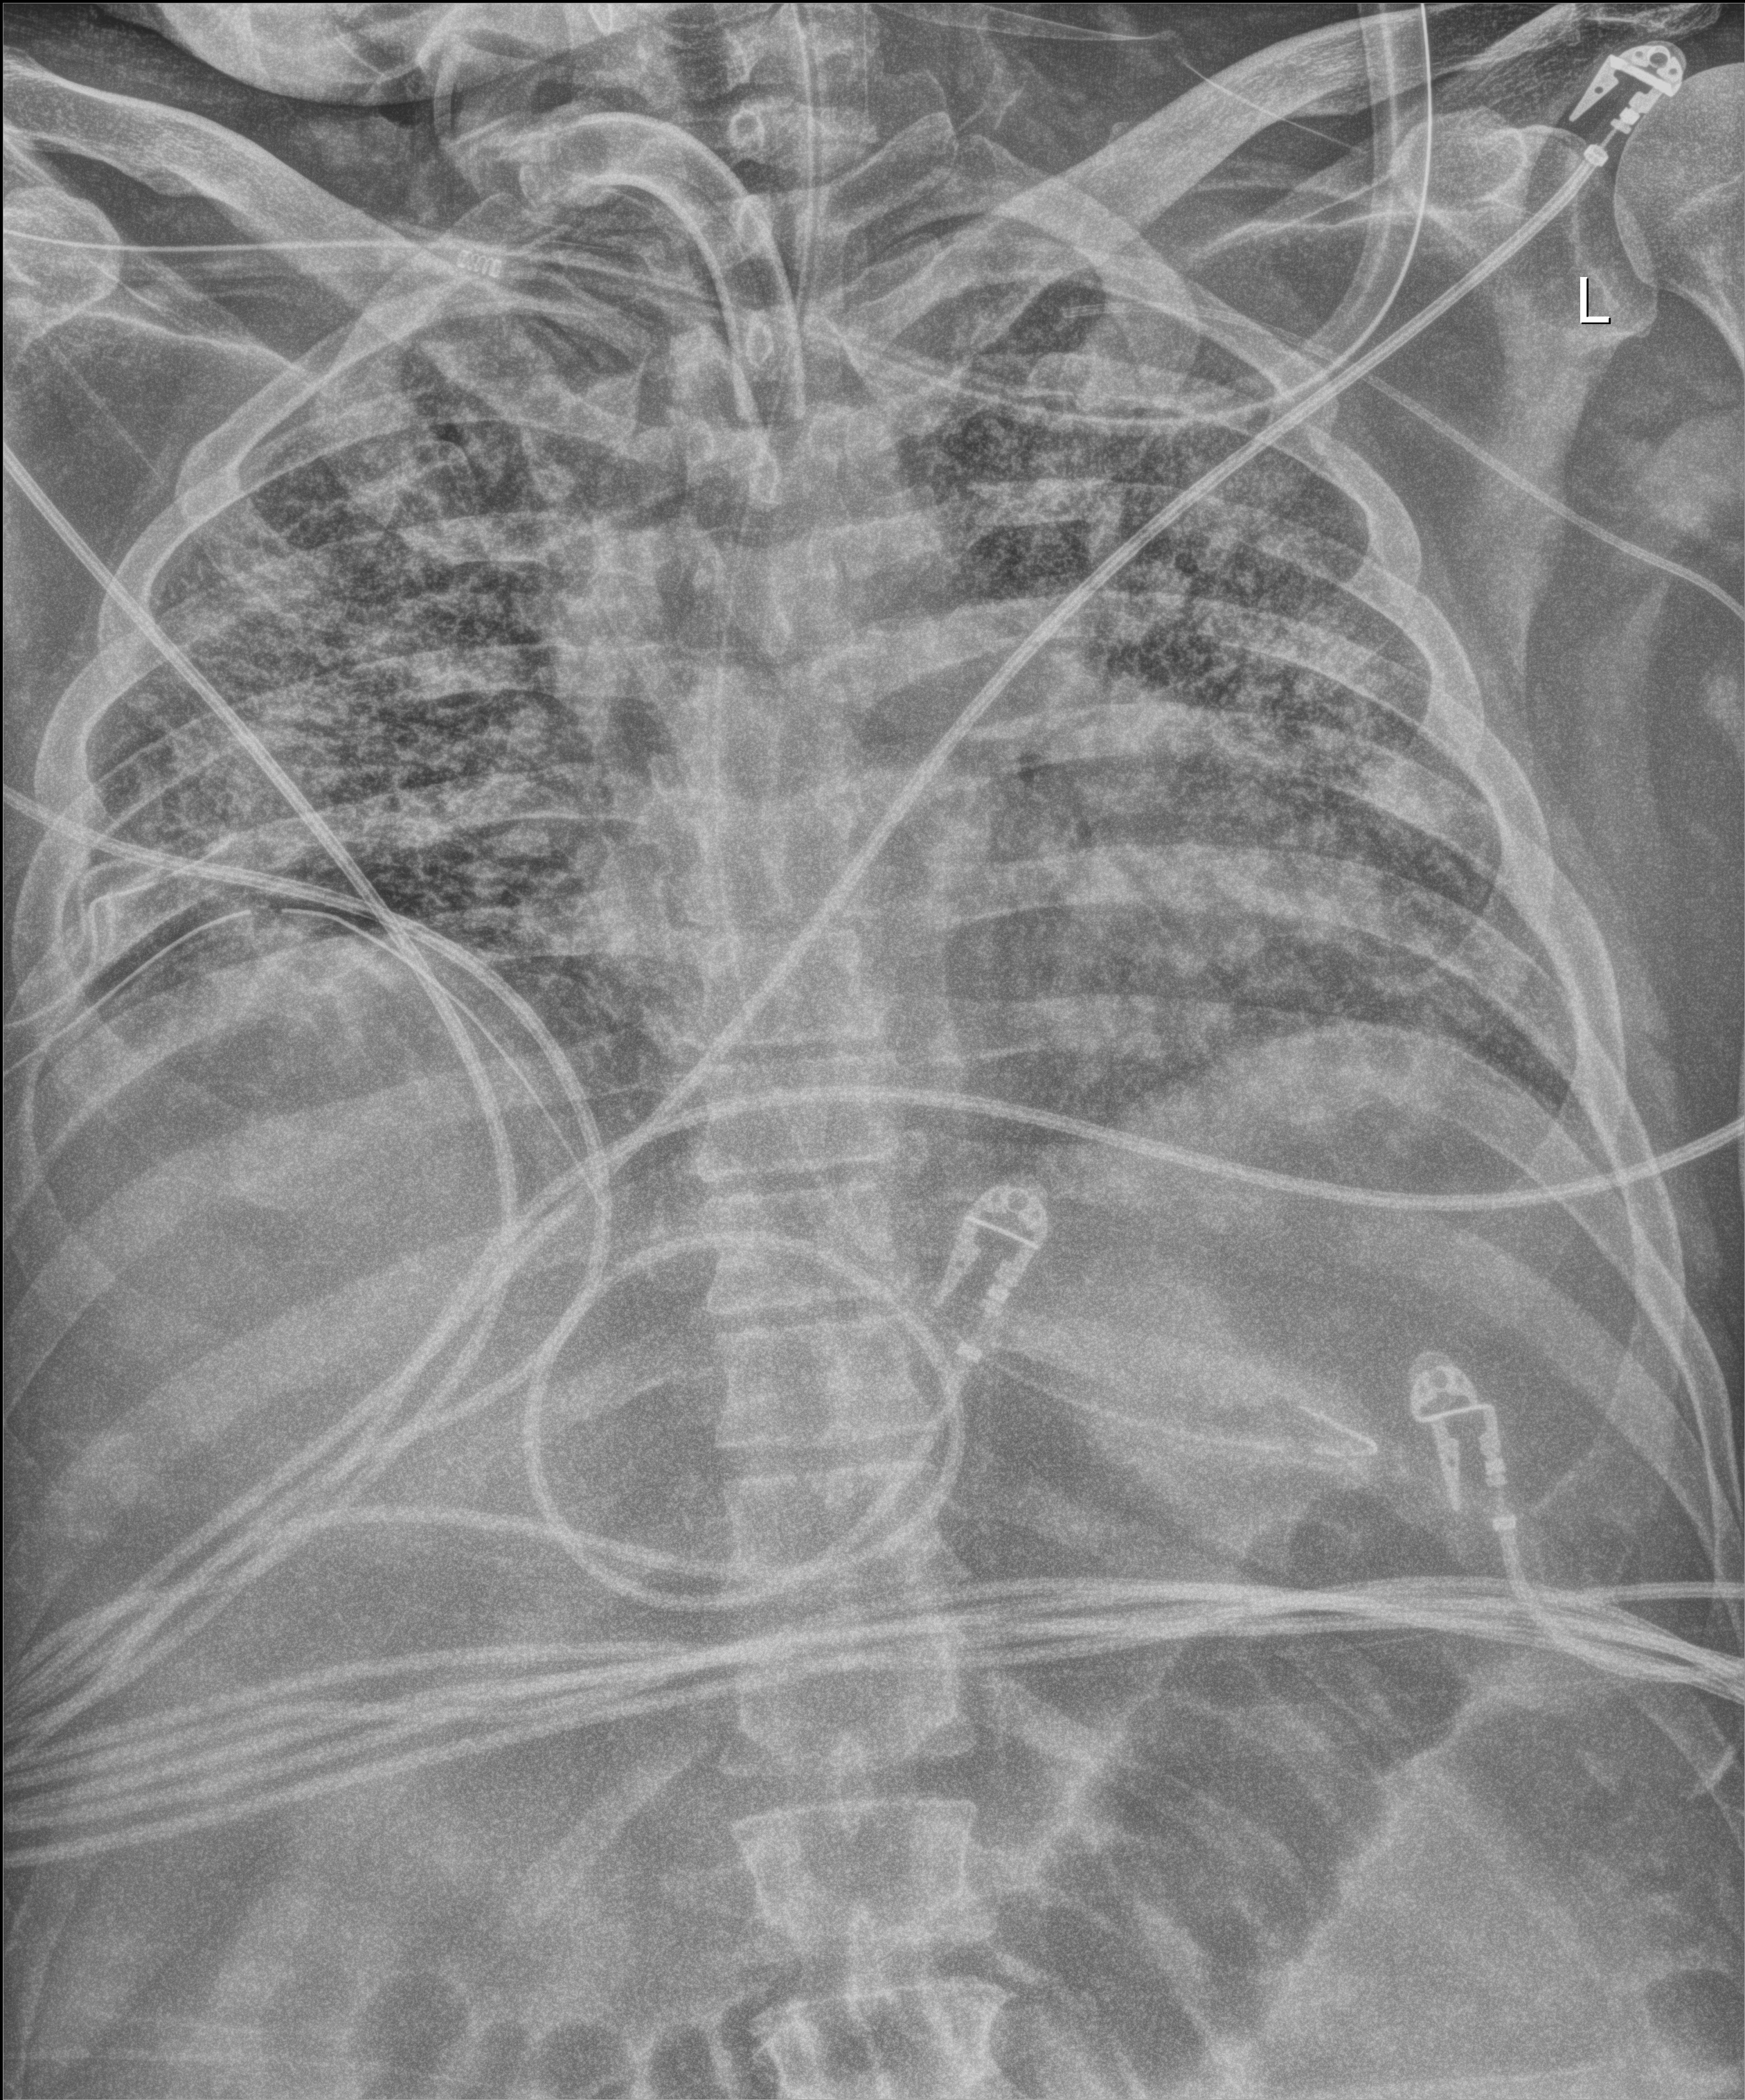
Bedside chest radiograph (digital radiography), anteroposterior (AP) projection. Patient hospitalised with COVID-19; male, aged 18–59 years.
Hospital-stay facts (about this admission, not read from this image; timing relative to this image not recorded): hypertension (admission record): yes; mechanically ventilated during this hospital stay: yes; admitted to intensive care during this hospital stay: yes.